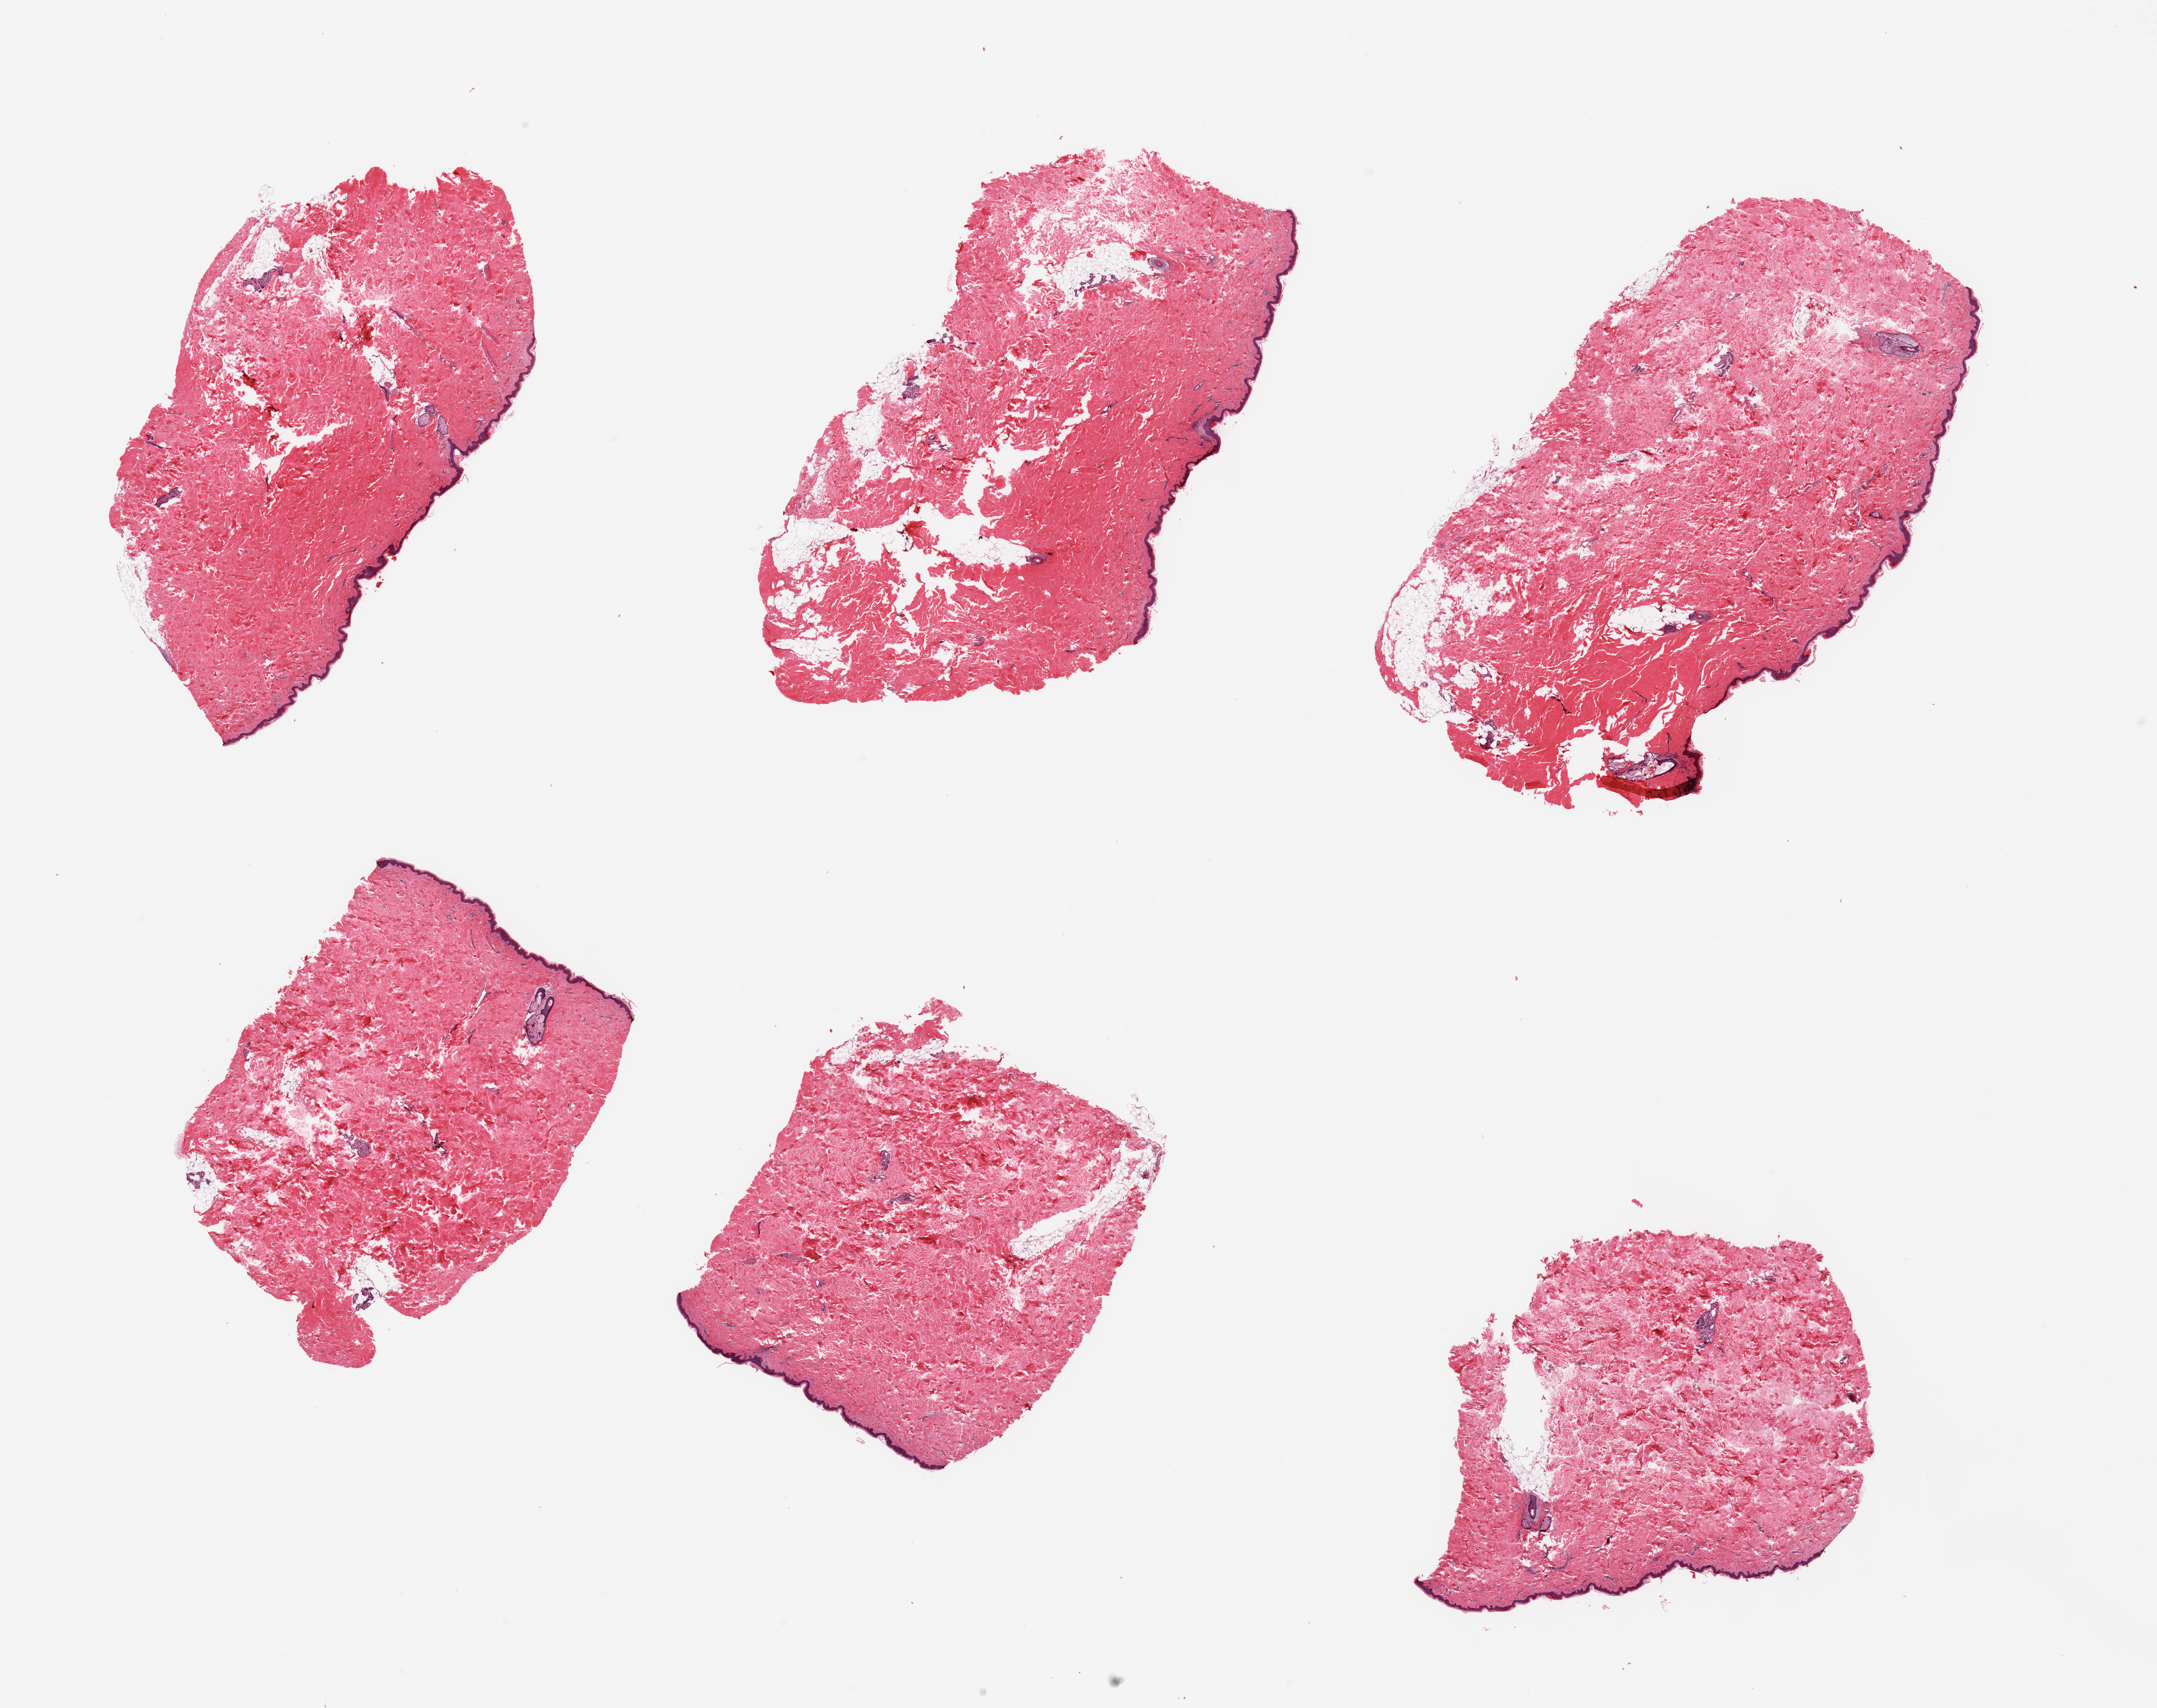
Haematoxylin and eosin whole-slide image, brightfield, a low-resolution overview of the entire scanned area, about 26.6 x 21.1 mm, PAXgene-fixed, paraffin-embedded tissue, target tissue: skin of suprapubic region, tissue donor sample. Donor sex: female.
Pathologist's review note for this sample: 6 pieces; essentially well trimmed with small component of internal fat.